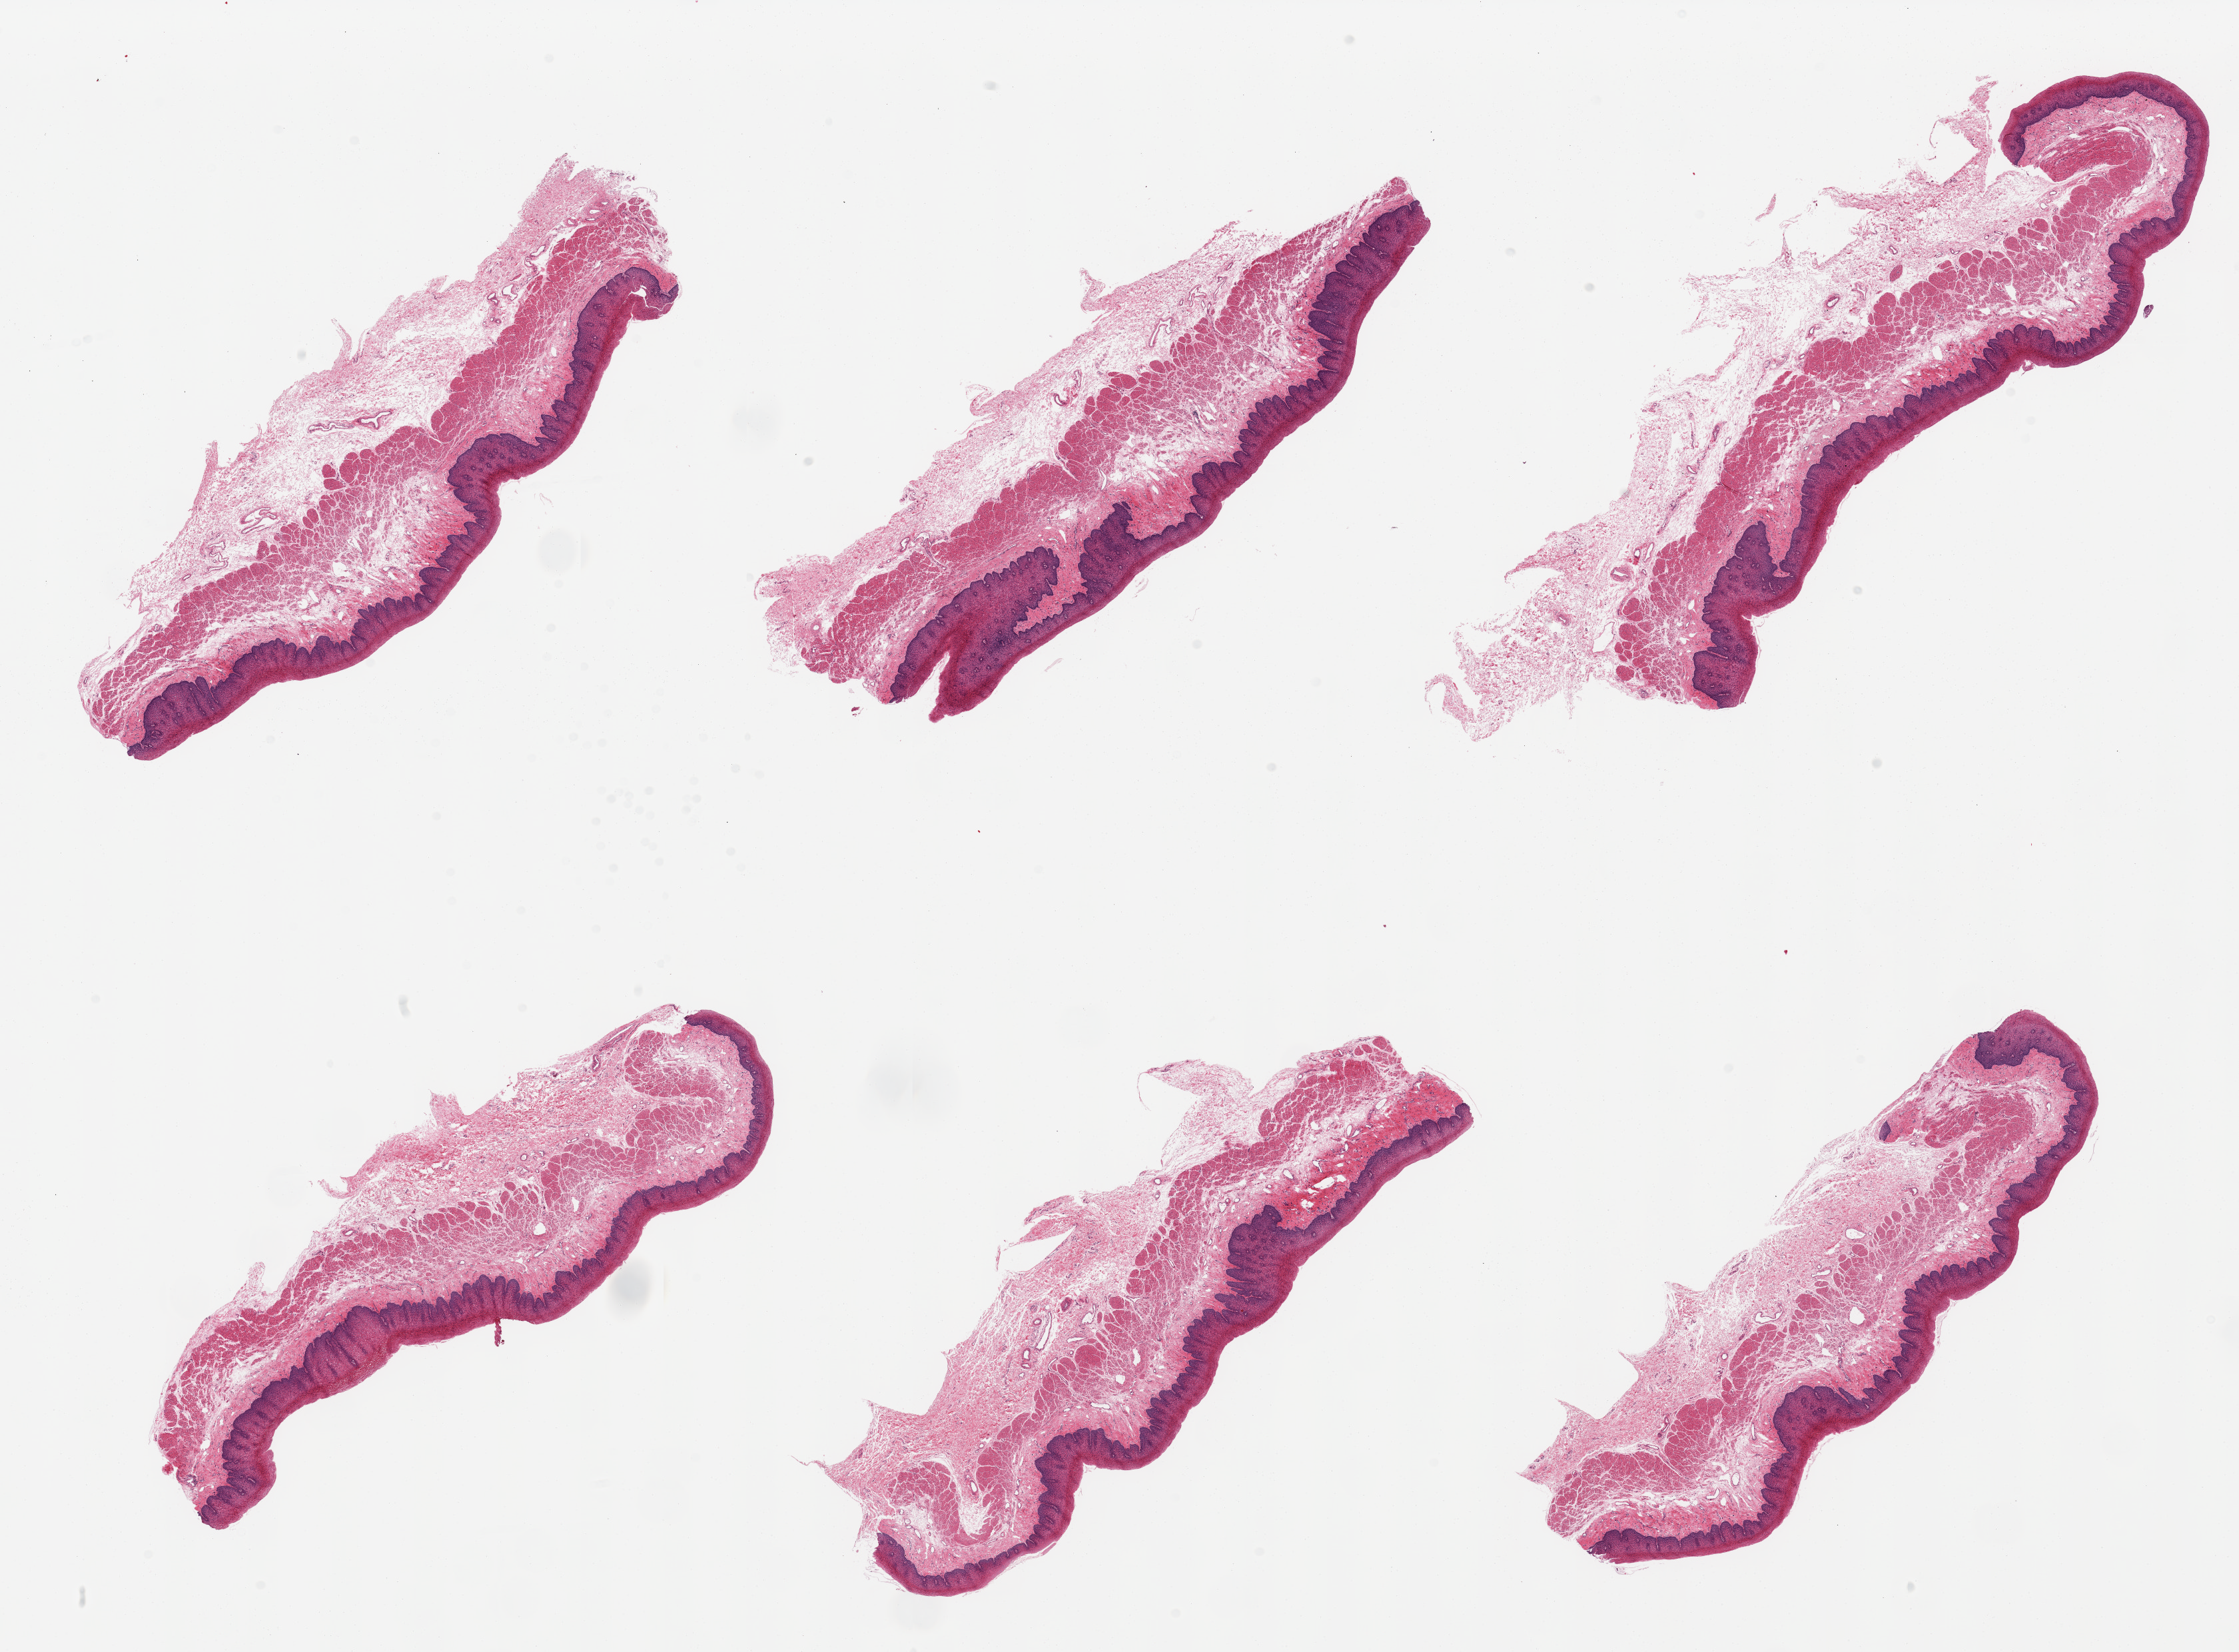
Haematoxylin and eosin whole-slide image, brightfield, whole scanned area (about 26.6 x 19.6 mm, slide scanned at 20x) shown as a low-resolution overview; PAXgene-fixed, paraffin-embedded tissue; sampled site (target tissue): esophageal mucous membrane; tissue donor sample.
Reviewer comment on this tissue sample: 6 pieces, squamous mucosa is ~0.5mm, ~20-25% thickness.